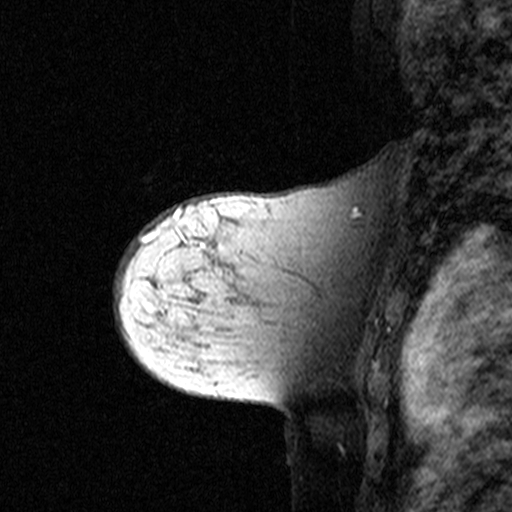
Breast MRI (dynamic contrast-enhanced), one sagittal slice; position 31 of 44 along the scan axis; dynamic contrast-enhanced study with each time point stored as its own series, time point 2 of 3 at this slice position (early post-contrast, ordered by acquisition time); 1.5 T; TE 4.5 ms, TR 11 ms; 3 mm slice thickness; 512 × 512 image matrix, field of view 200 × 200 mm. Female patient, age 44 years. From the clinical record (not read from this slice): setting: breast cancer imaged before/during neoadjuvant chemotherapy; receptor status: triple-negative.
Outlined on this slice (semi-automatically segmented with operator editing):
- analysis volume of interest (the breast-tissue region the enhancement analysis was run in; not a lesion): bounding box <142,208,349,363> (left, top, right, bottom; pixels)
- tumour enhancement mask (voxels above the 90 % enhancement threshold inside the analysis volume of interest): <142,208,182,242>